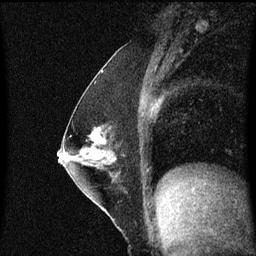
Breast MRI (dynamic contrast-enhanced), one sagittal slice; position 28 of 60 along the scan axis; dynamic contrast-enhanced series, image 2 of 3 at this slice position (ordered by acquisition); 1.5 T; TE 4.2 ms, TR 8.4 ms; 2 mm slice thickness; 256 × 256 image matrix. Female patient, age 52 years. Case-level facts recorded for this patient, not image findings: setting: breast cancer imaged before/during neoadjuvant chemotherapy; receptor status: HER2-positive.
Outlined on this slice (semi-automatically segmented with operator editing):
- analysis volume of interest (the breast-tissue region the enhancement analysis was run in; not a lesion): box from (x=71, y=118) to (x=122, y=187) px
- tumour enhancement mask (voxels above the 70 % enhancement threshold inside the analysis volume of interest): (x=91, y=130)–(x=106, y=143)